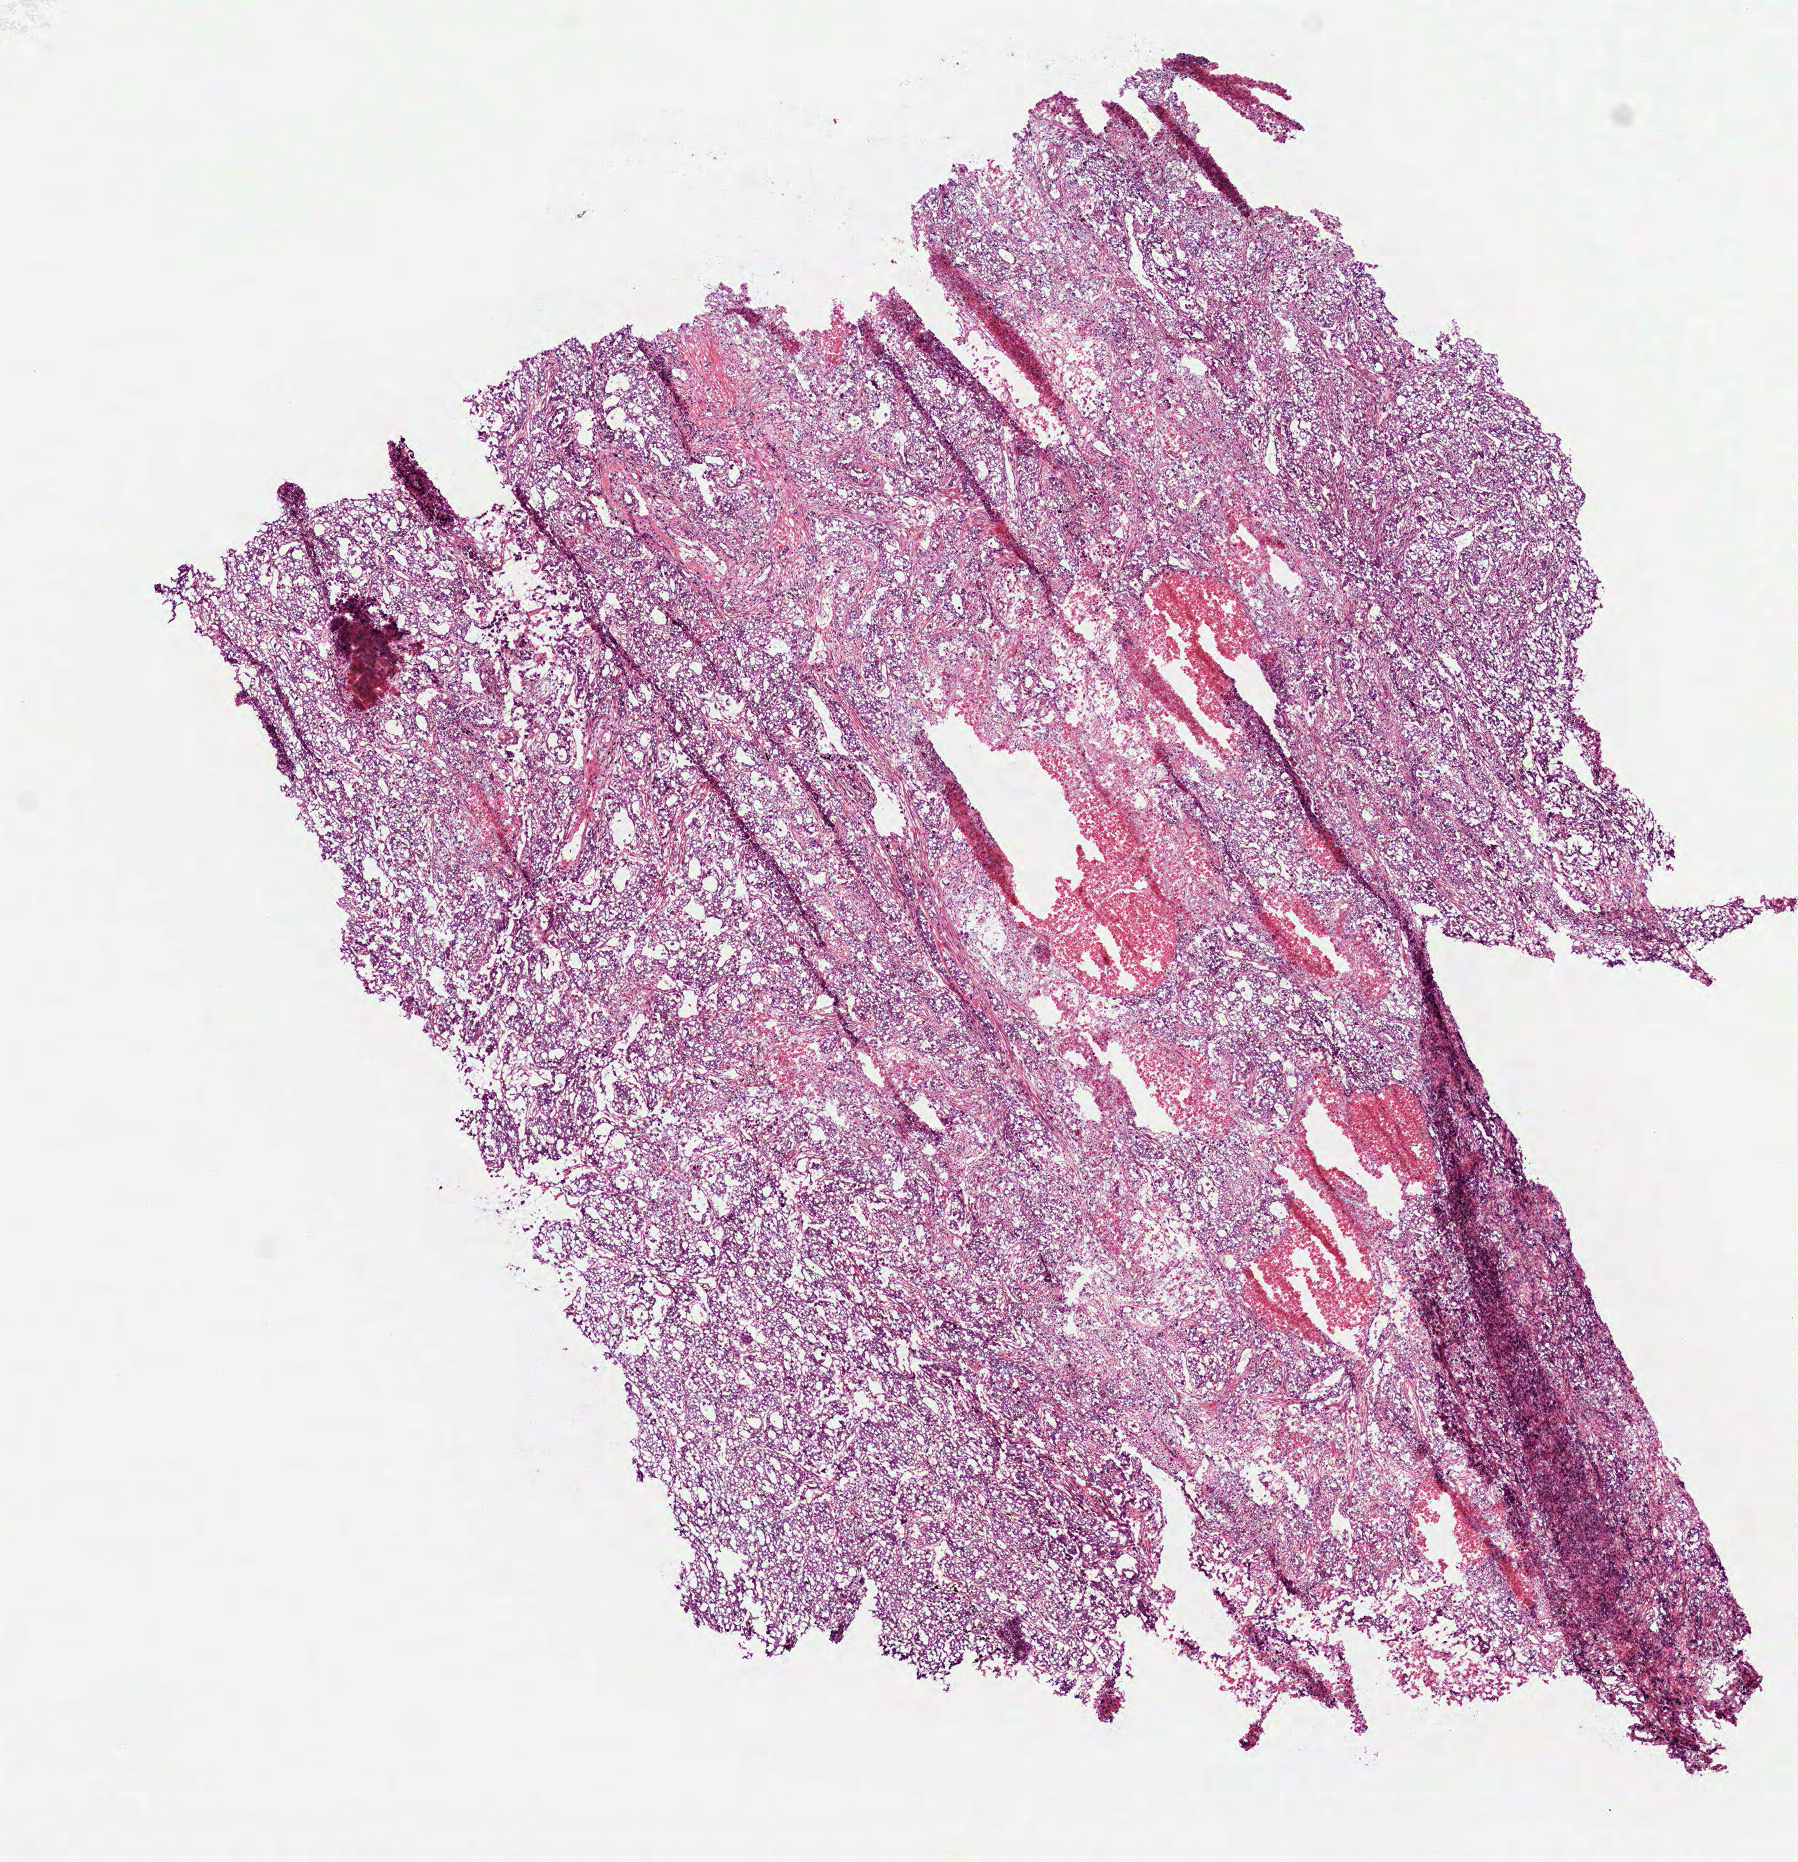
Whole-slide histology image, H&E, a low-resolution overview of the entire scanned area, about 7.3 x 7.5 mm (acquisition: 40x scan), frozen section, lung, primary tumour sample. Male, age 59 years at initial diagnosis. Pathologist review of this section (percent, as recorded): tumour cells 75%, tumour nuclei 80%, normal cells 0%, stromal cells 10%, necrosis 15%.
* AJCC pathologic stage: IIB (6th edition)
* laterality: left
* histologic diagnosis: Adenocarcinoma, NOS (lower lobe, lung)